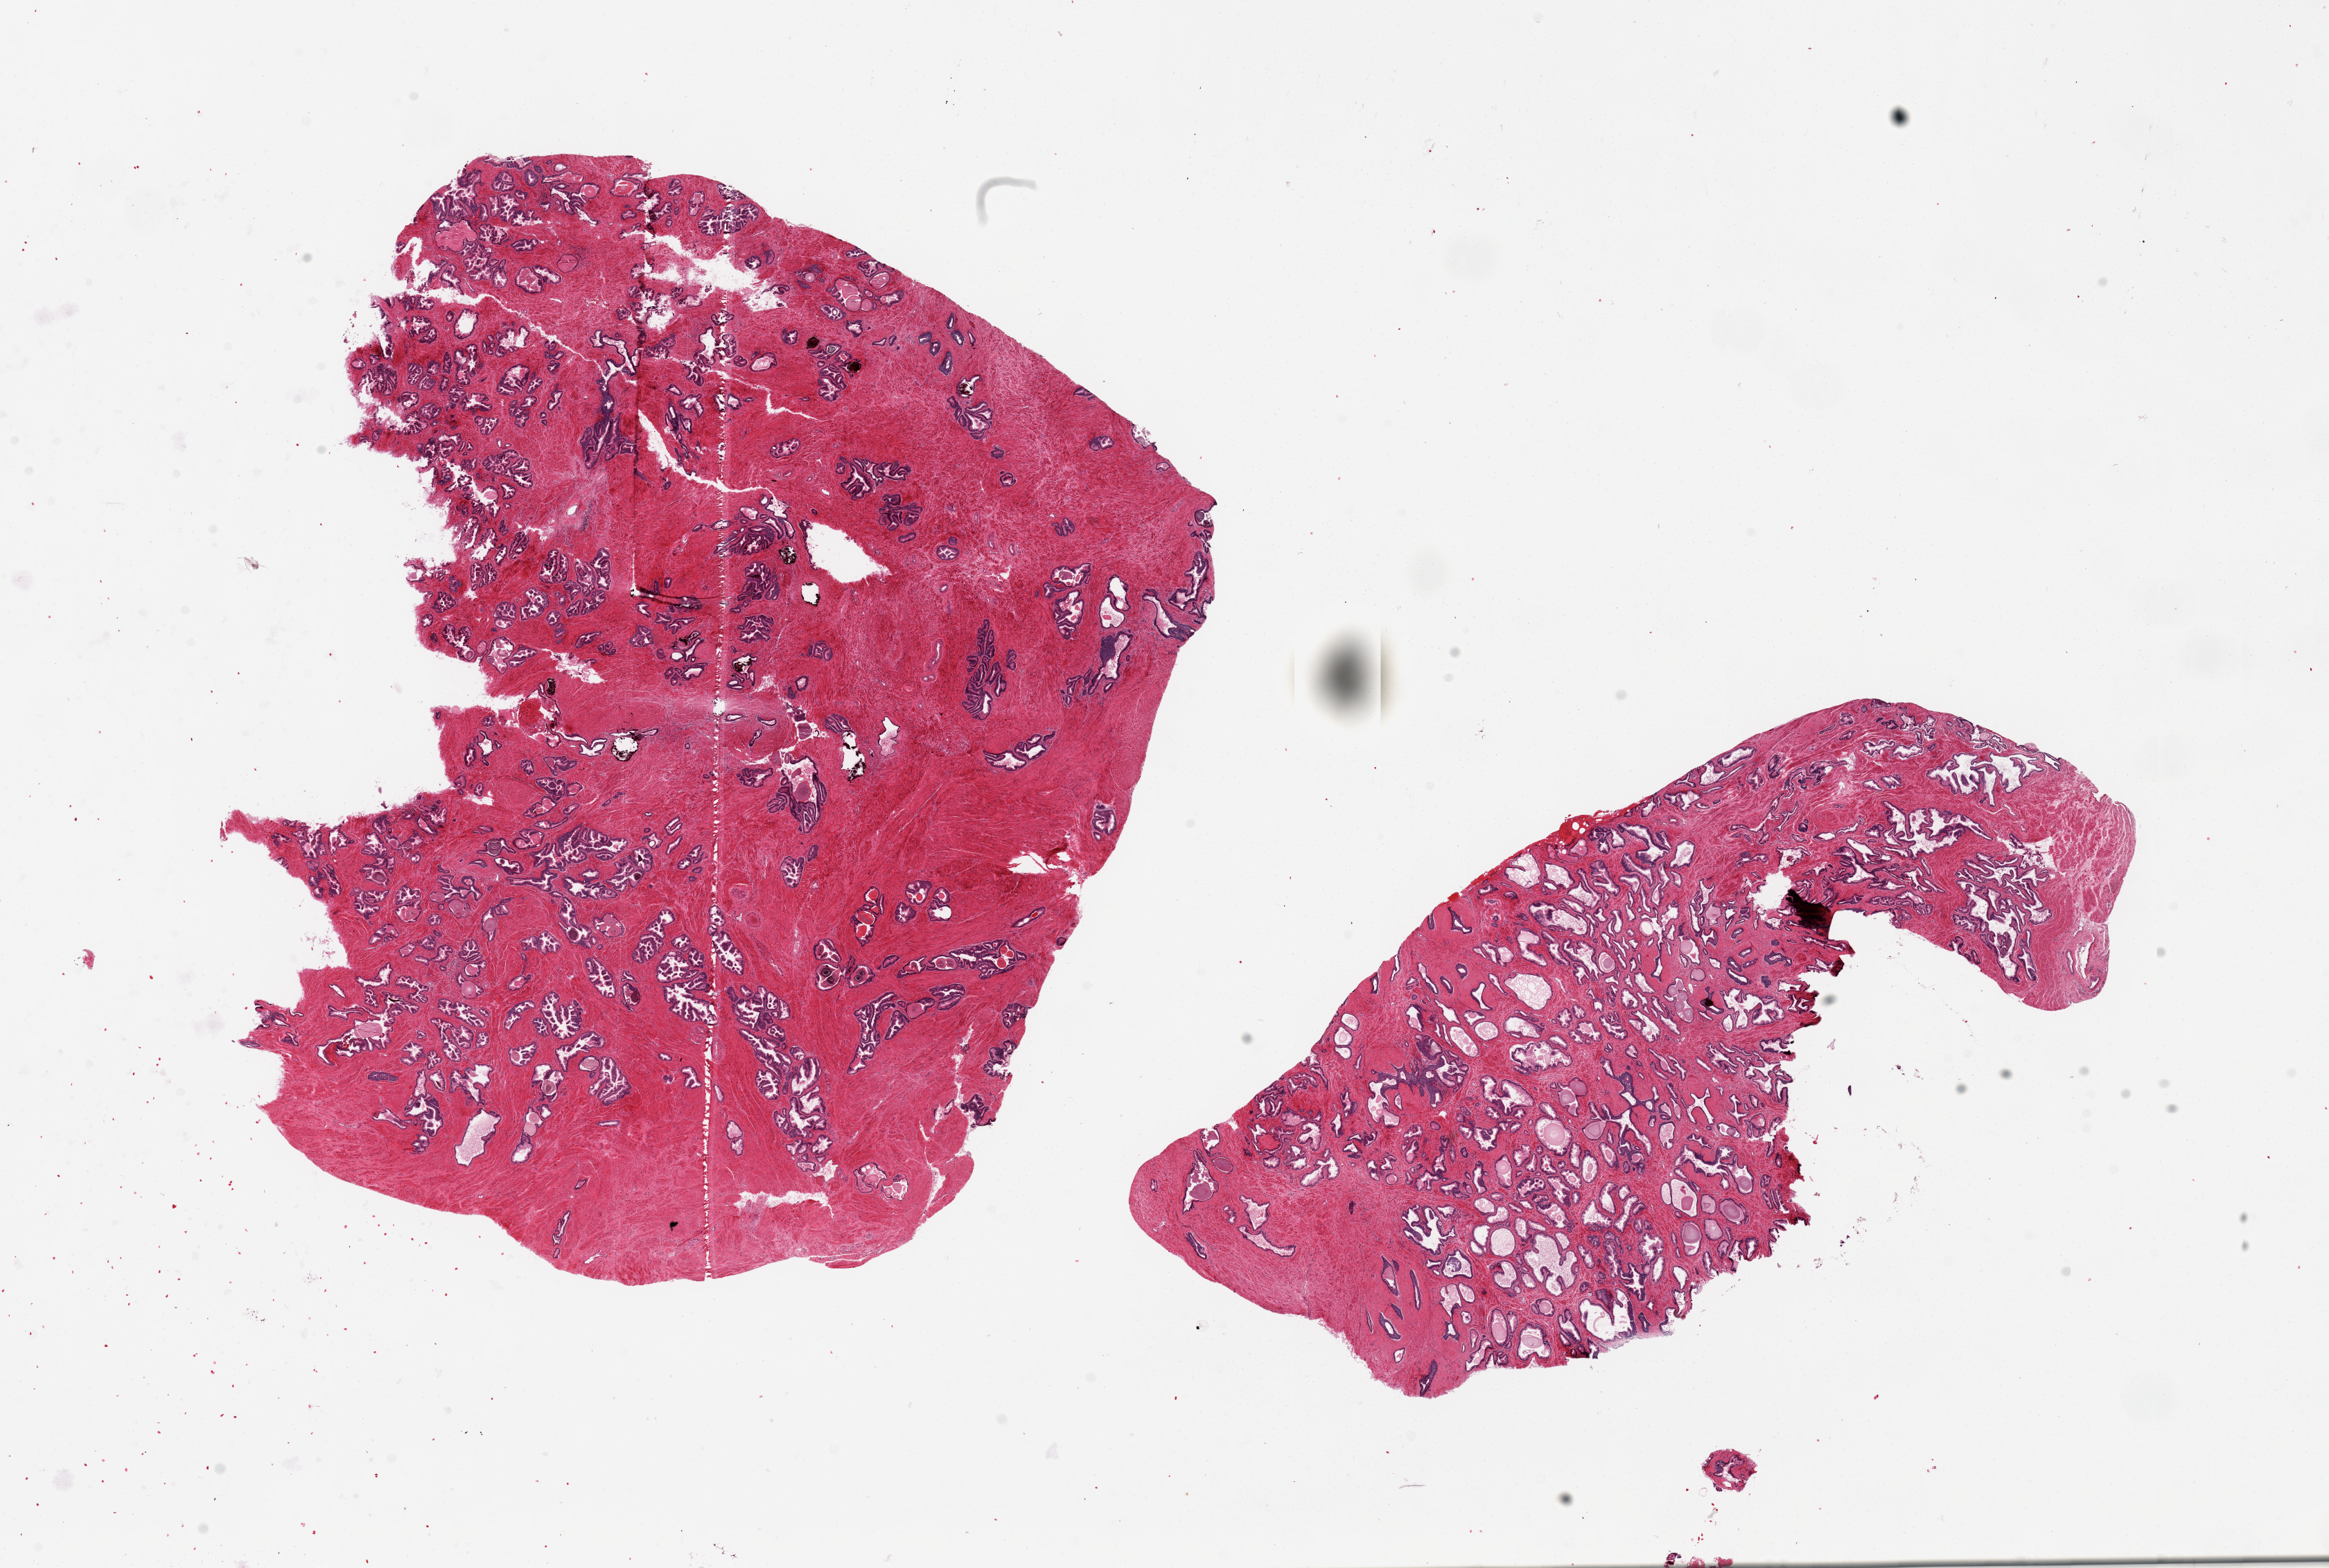
Whole-slide image, H&E stain, brightfield, low-resolution overview of the scanned area, about 26.6 x 17.9 mm (slide scanned at 20x). PAXgene-fixed paraffin-embedded (PFPE) section. Section of prostate (target tissue). Tissue donor sample. Donor: male.
Reviewer comment on this tissue sample: 2 pieces, 12x10 and 11.5x5mm; mild hyperplasia.